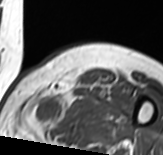
MRI of an extremity soft-tissue mass, one axial slice. Position 50 of 65 along the scan axis. MR volume resampled by the dataset authors to the PET/CT grid (not the native acquisition matrix). 3.27 mm slice thickness. 163 × 155 image matrix, field of view 159 × 151 mm. Female patient. From the clinical record (not read from this slice): histological type: pleomorphic leiomyosarcoma; grade: high; site of the primary tumour: left thigh.
Annotated regions visible in this slice (expert contour drawn on MRI and transferred to this co-registered scan by the dataset authors):
- gross tumour volume including surrounding oedema: box from (x=28, y=90) to (x=88, y=134) px